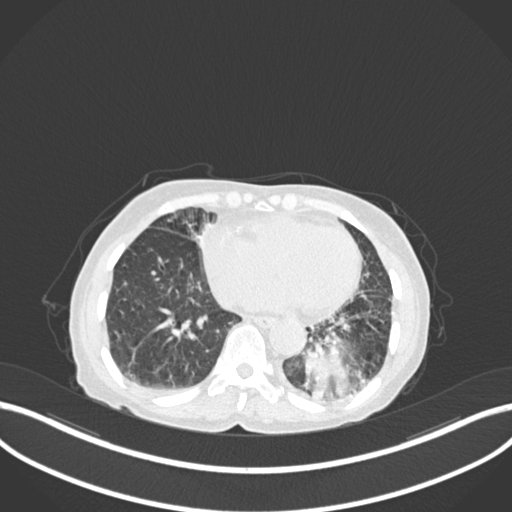
Chest CT, one axial slice; reconstruction kernel B30f; 120 kVp; lung window (W 1500 / L -600 HU); 512 × 512 image matrix, field of view 400 × 400 mm. Patient: female, 78 years. Case-level facts recorded for this patient, not image findings: clinical TNM (as recorded): T3 N0 M1.
Outlined on this slice (rectangle marked by the reading radiologist):
- lung tumour (recorded histology: squamous cell carcinoma): bounding box <298,332,361,406> (left, top, right, bottom; pixels)